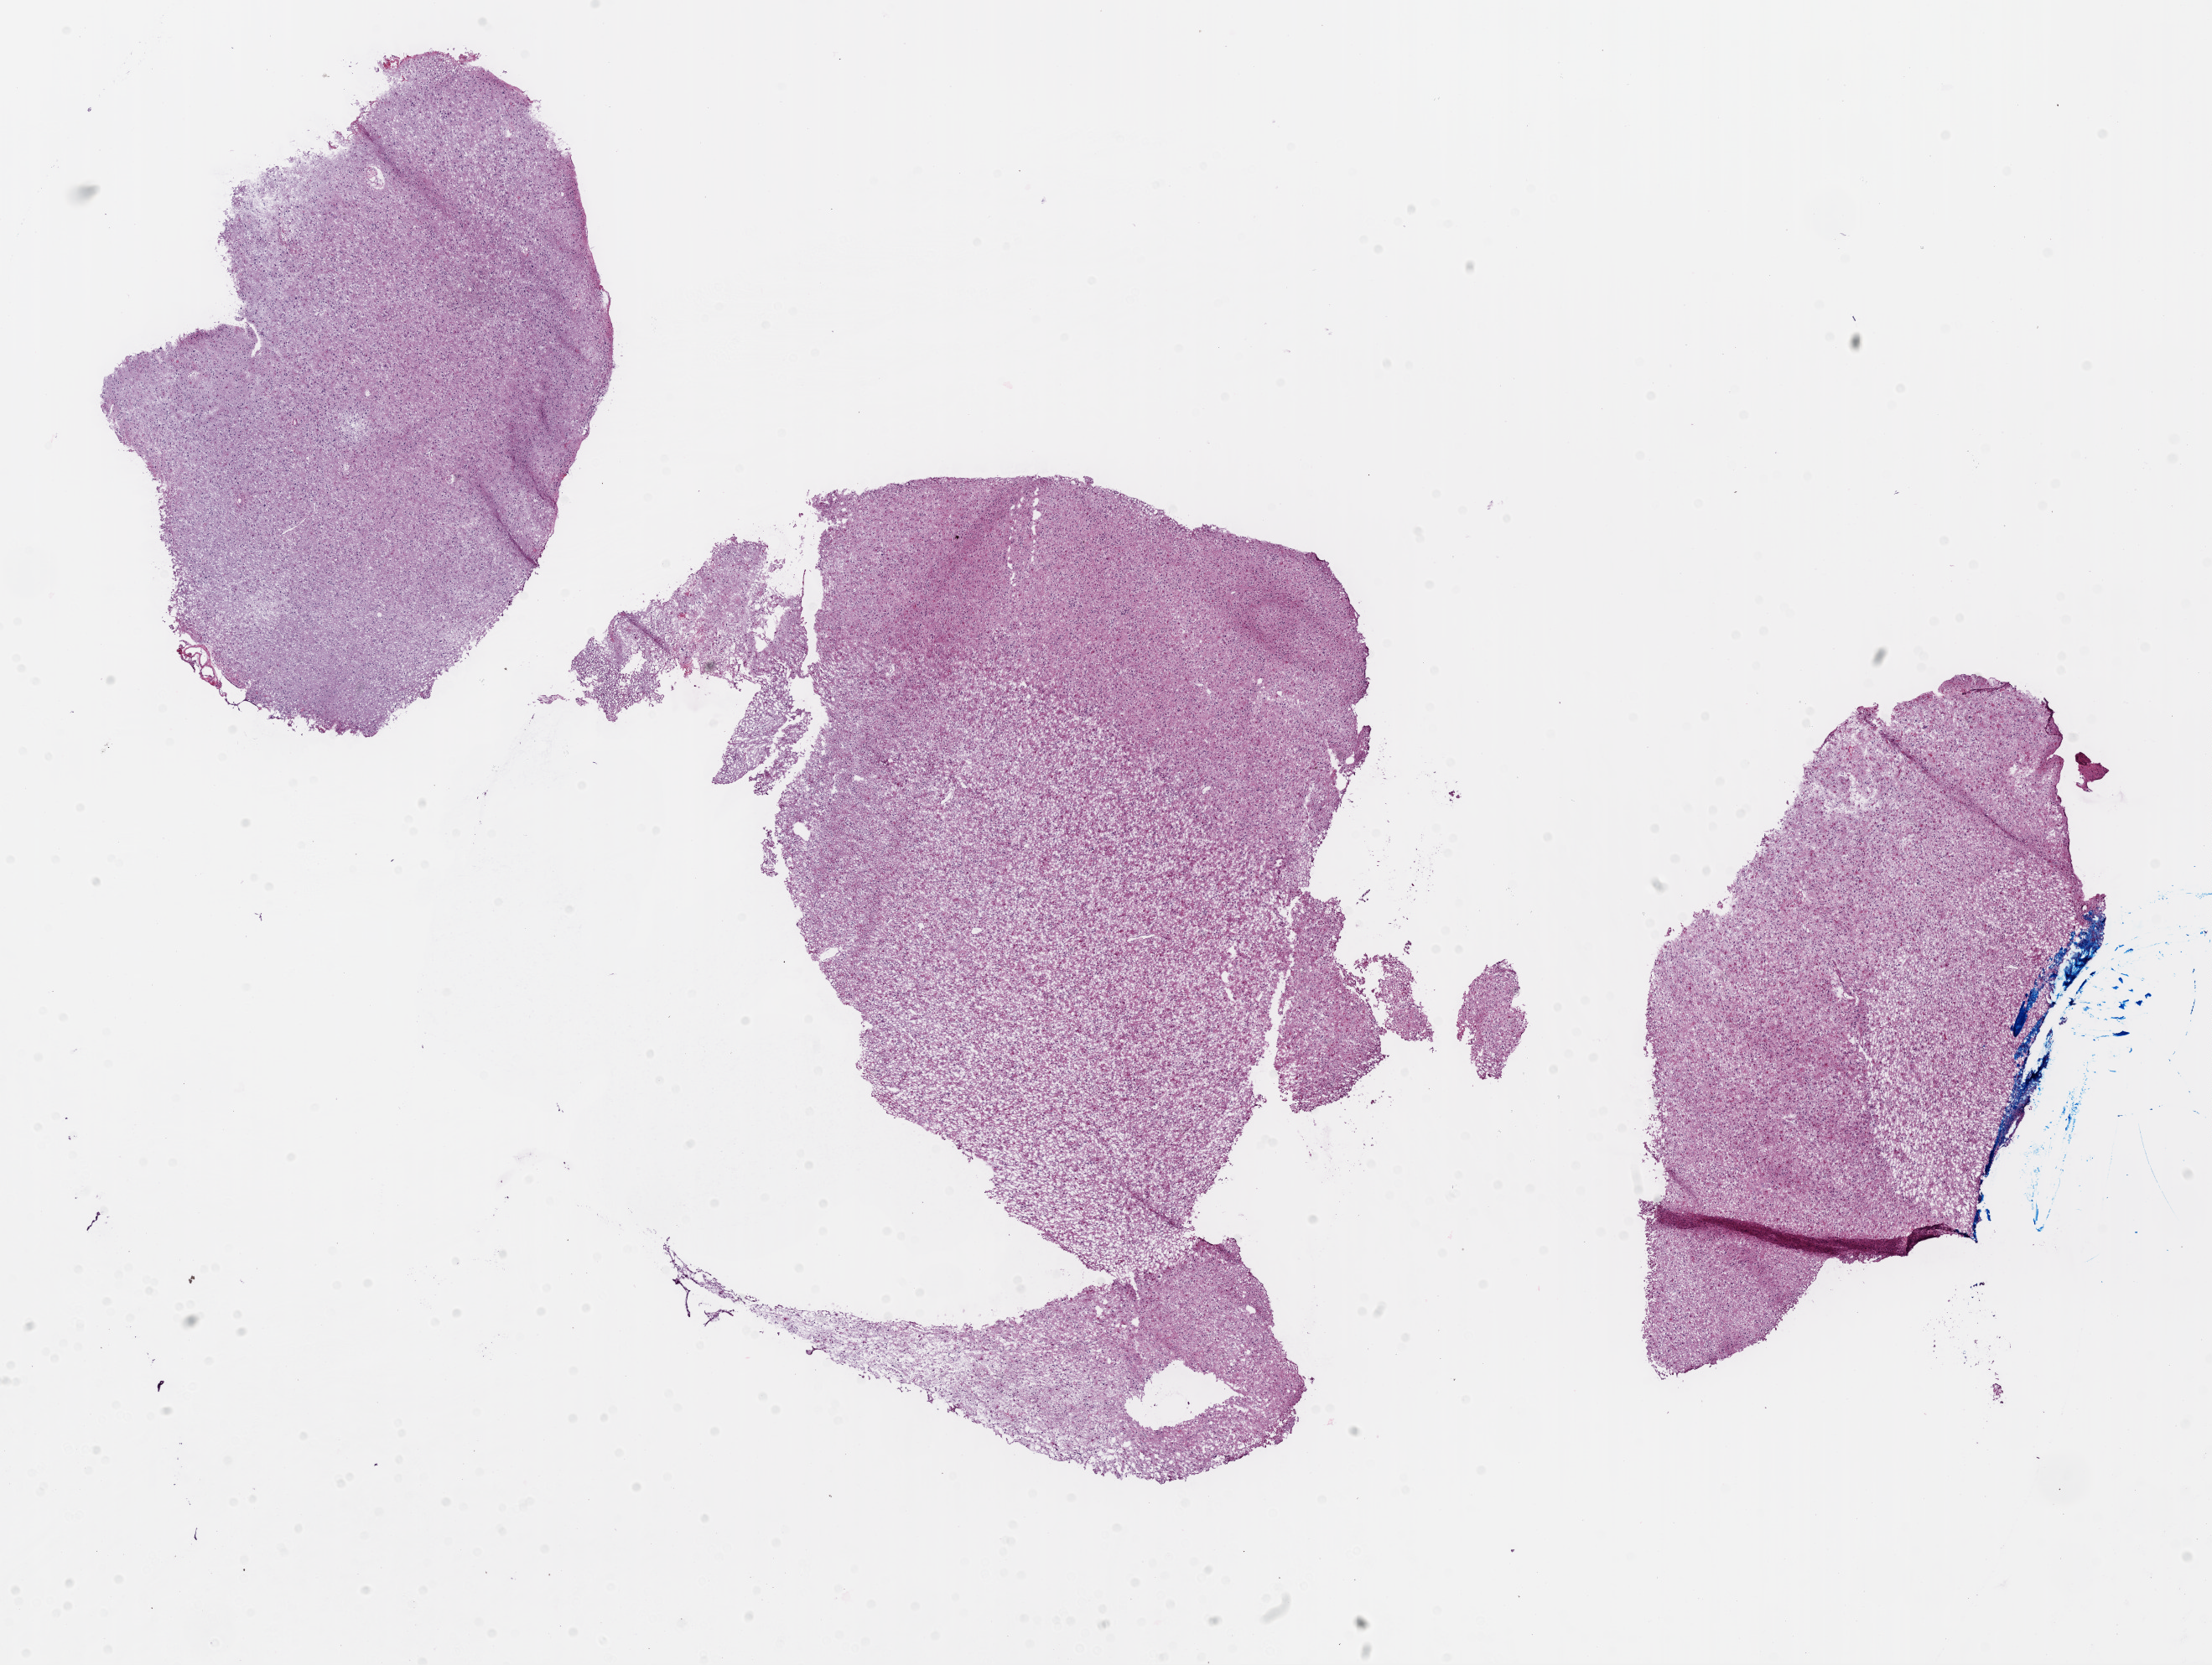
Digitized H&E tissue section (whole slide), low-resolution overview of the scanned area, about 21.3 x 16.0 mm (from a 20x scan), frozen section from the top of the tissue portion, primary tumour sample from the brain. Male patient; age at initial diagnosis 85 years. Pathologist review of this section (percent, as recorded): tumour cells 85%, tumour nuclei 85%, normal cells 10%, stromal cells 5%, necrosis 0%.
- histologic diagnosis: Glioblastoma